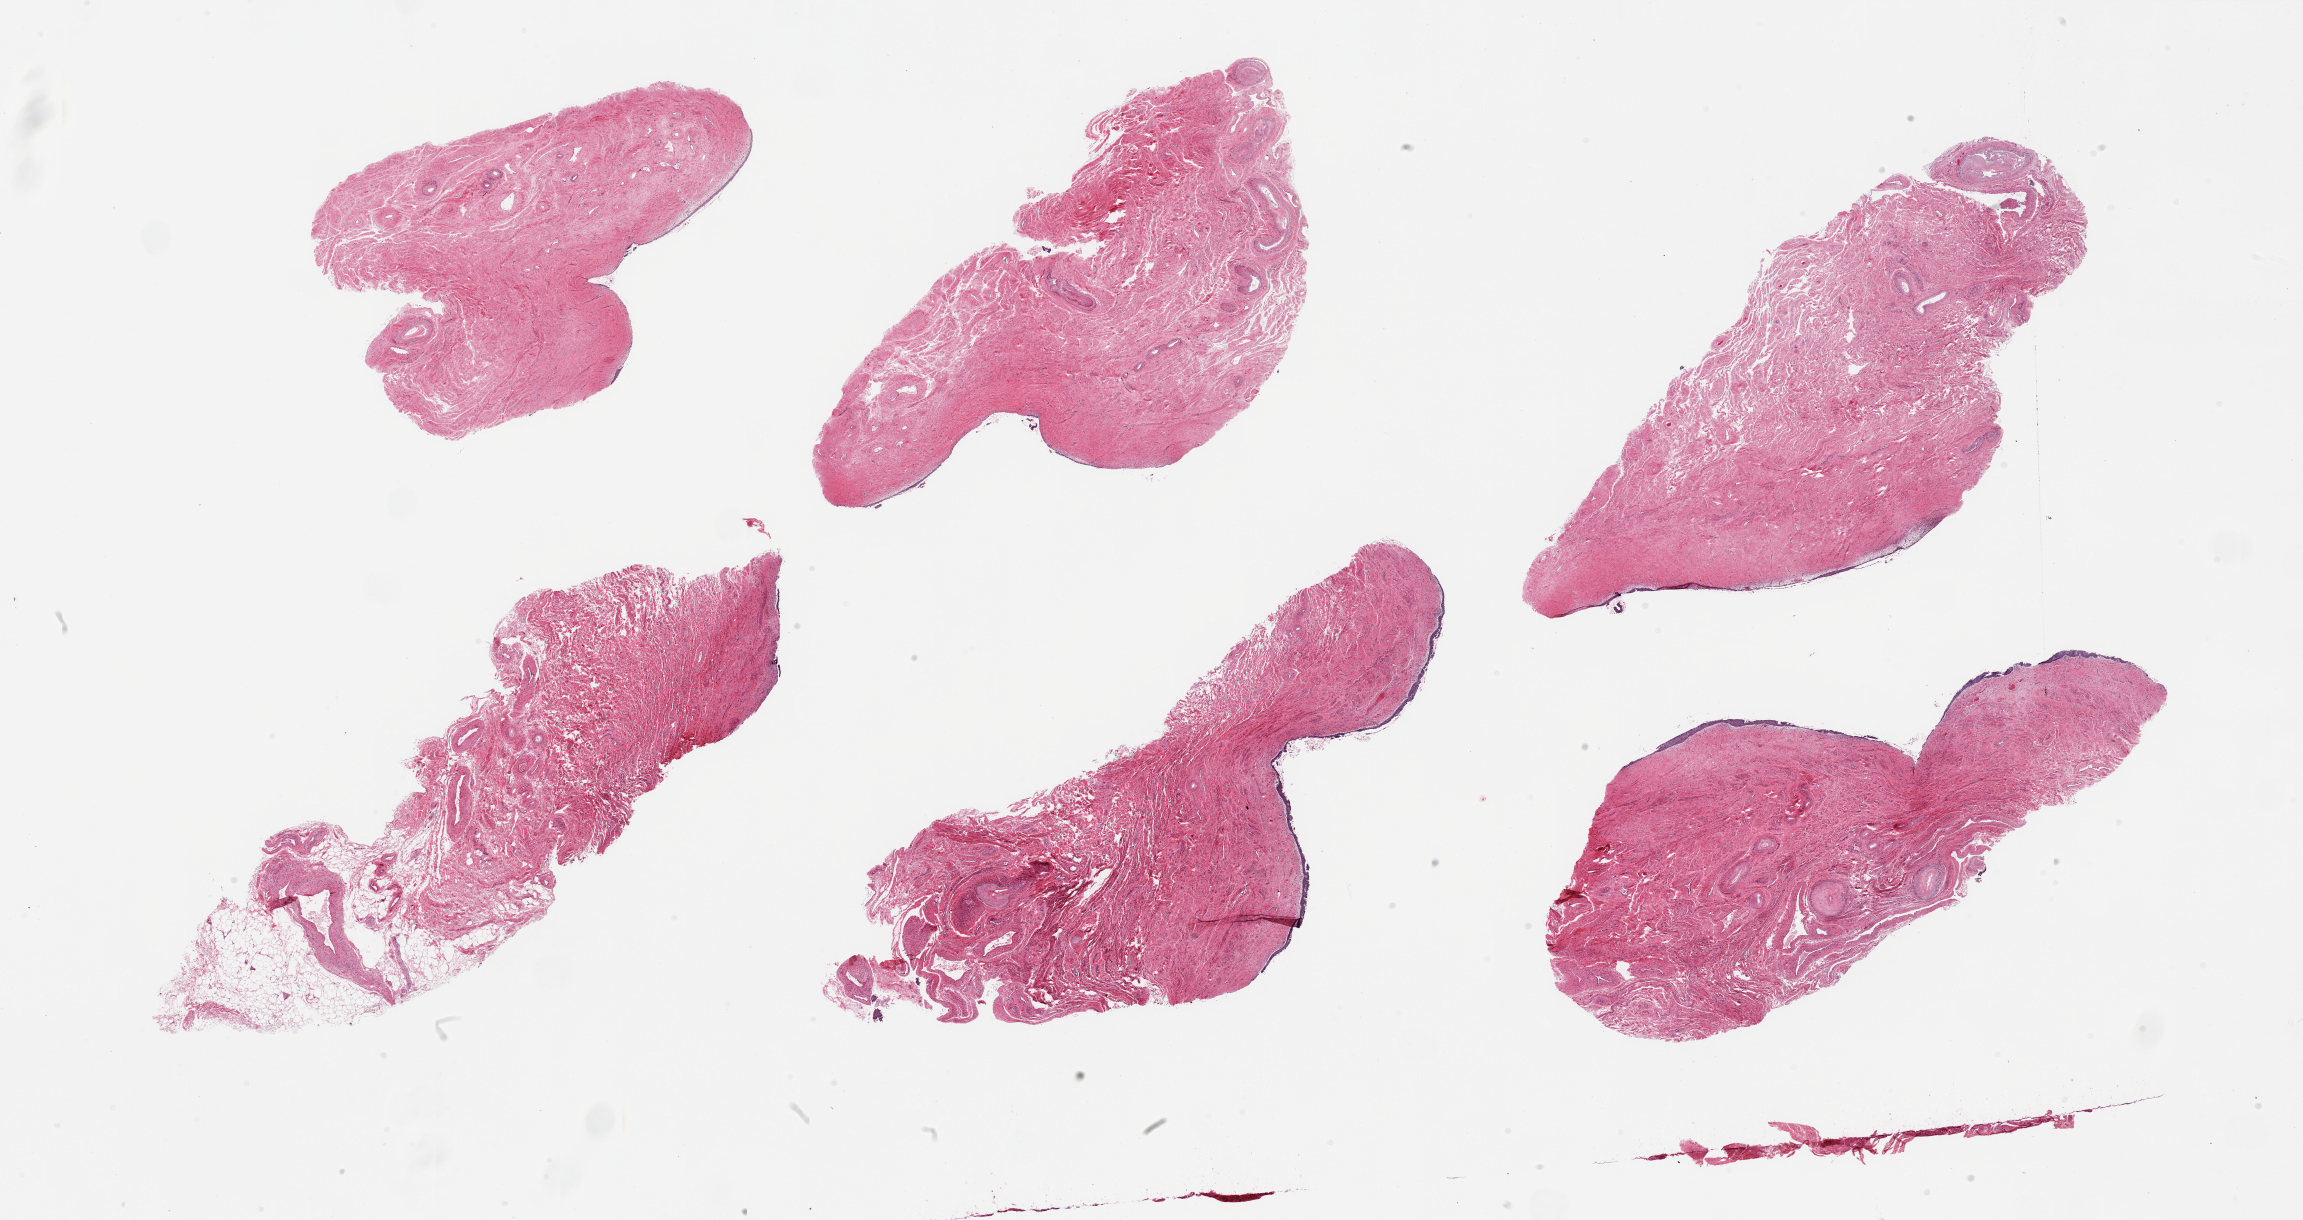
Whole-slide image, hematoxylin and eosin (H&E) stain, low-resolution overview of the scanned area, about 36.4 x 19.3 mm (acquisition: 20x scan), PAXgene-fixed, paraffin-embedded tissue, section of vagina (target tissue), donor tissue sample. Donor: female.
Reviewer comment on this tissue sample: 6 pieces; atrophic, largely sloughed epithelium.